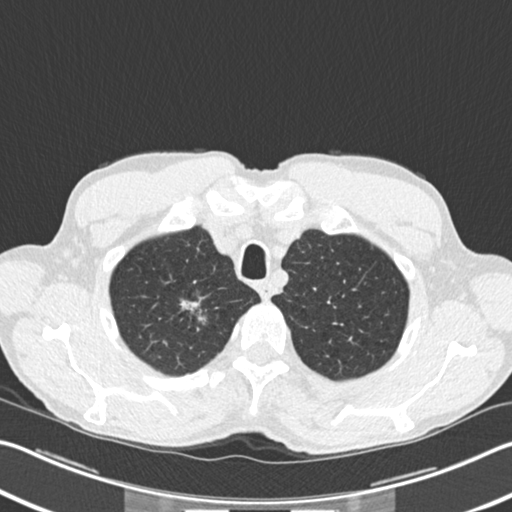
Low-dose screening chest CT, axial slice, second screening round (one year after baseline), lung window (W 1500 / L -600 HU), 2 mm slice thickness, slice 31 of 220 in the series. Male participant, aged 62 years at enrolment. Former smoker at enrolment.
• Lesion marked by an expert reader, bounding box [x1, y1, x2, y2] px = [173, 290, 214, 337].
• The screening reader recorded 2 non-calcified nodules or masses ≥4 mm on this exam (right upper lobe, right upper lobe); which of them this box marks is not recorded.
• Later outcome: lung cancer diagnosed 5 days after this screen — bronchiolo-alveolar adenocarcinoma, NOS, right upper lobe, well differentiated (G1), stage IA (AJCC 6th edition), 15 mm at pathology.